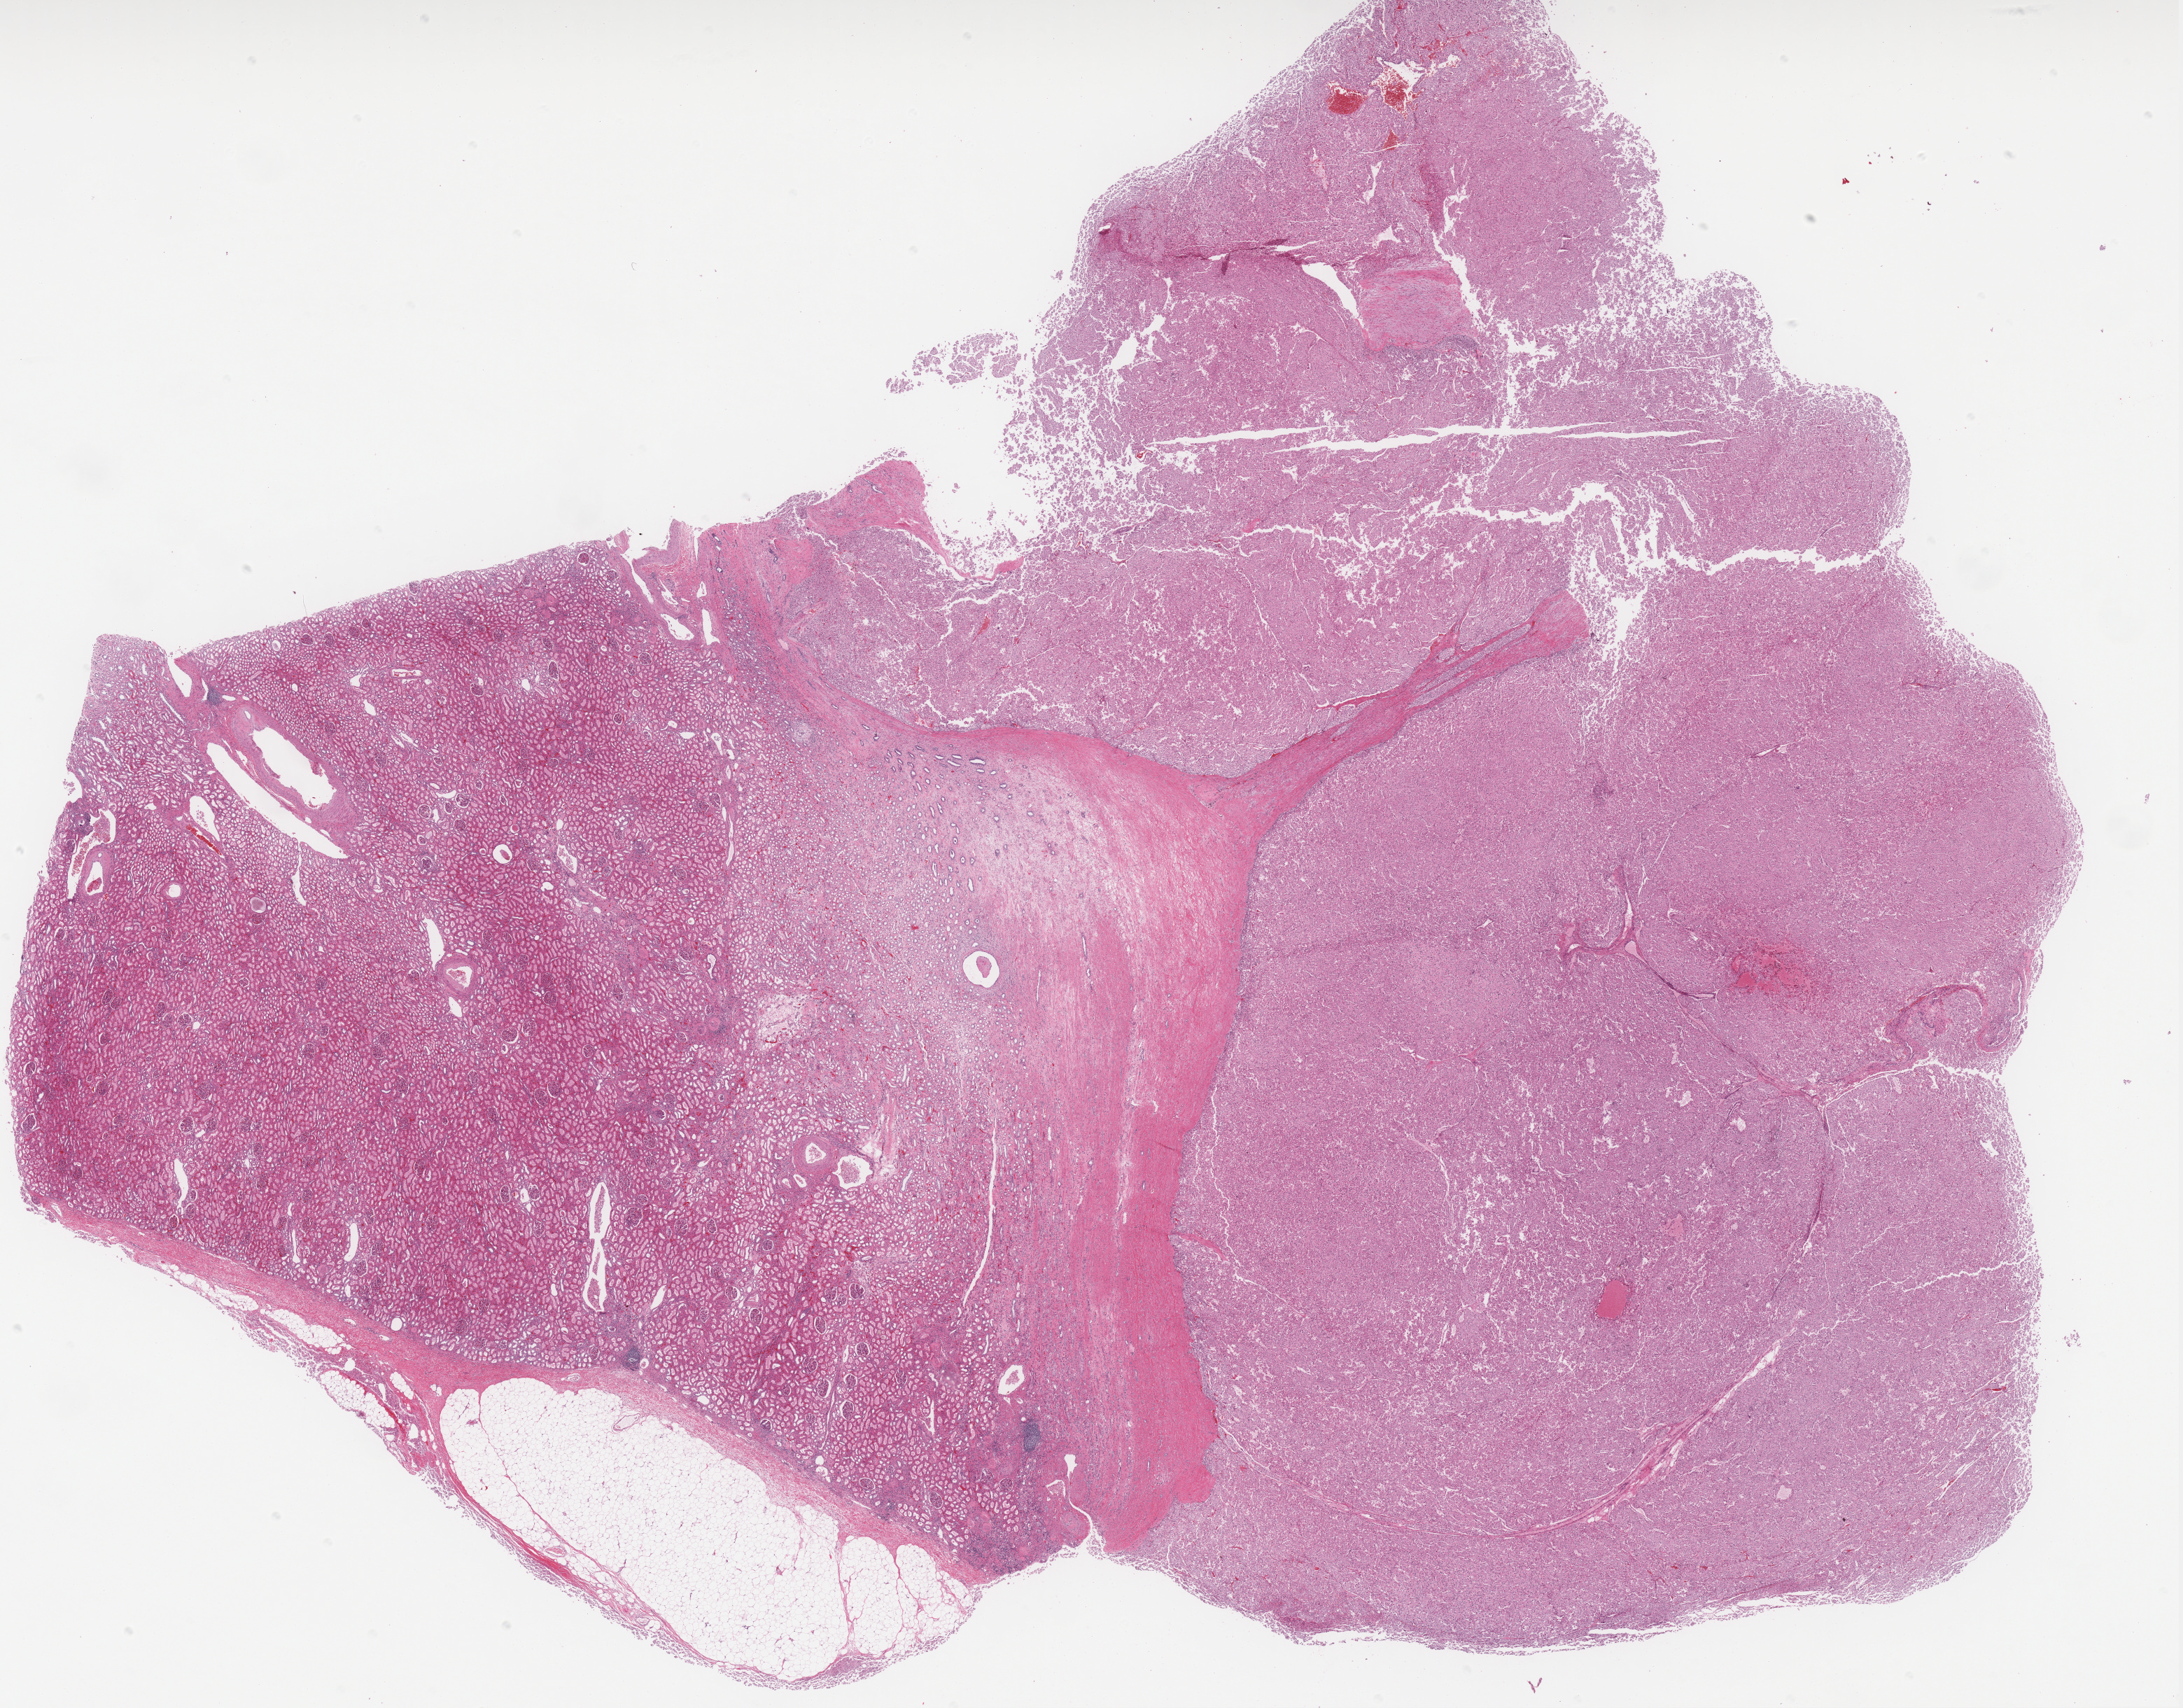
Whole-slide histology image, Hematoxylin and eosin (H&E) stained, a low-resolution overview of the entire scanned area, about 24.9 x 19.5 mm, FFPE section, sample: primary tumour, kidney. Female patient; age at initial diagnosis 44 years.
Histologic diagnosis: Renal cell carcinoma, chromophobe type. Laterality: right. AJCC pathologic stage: II (6th edition).